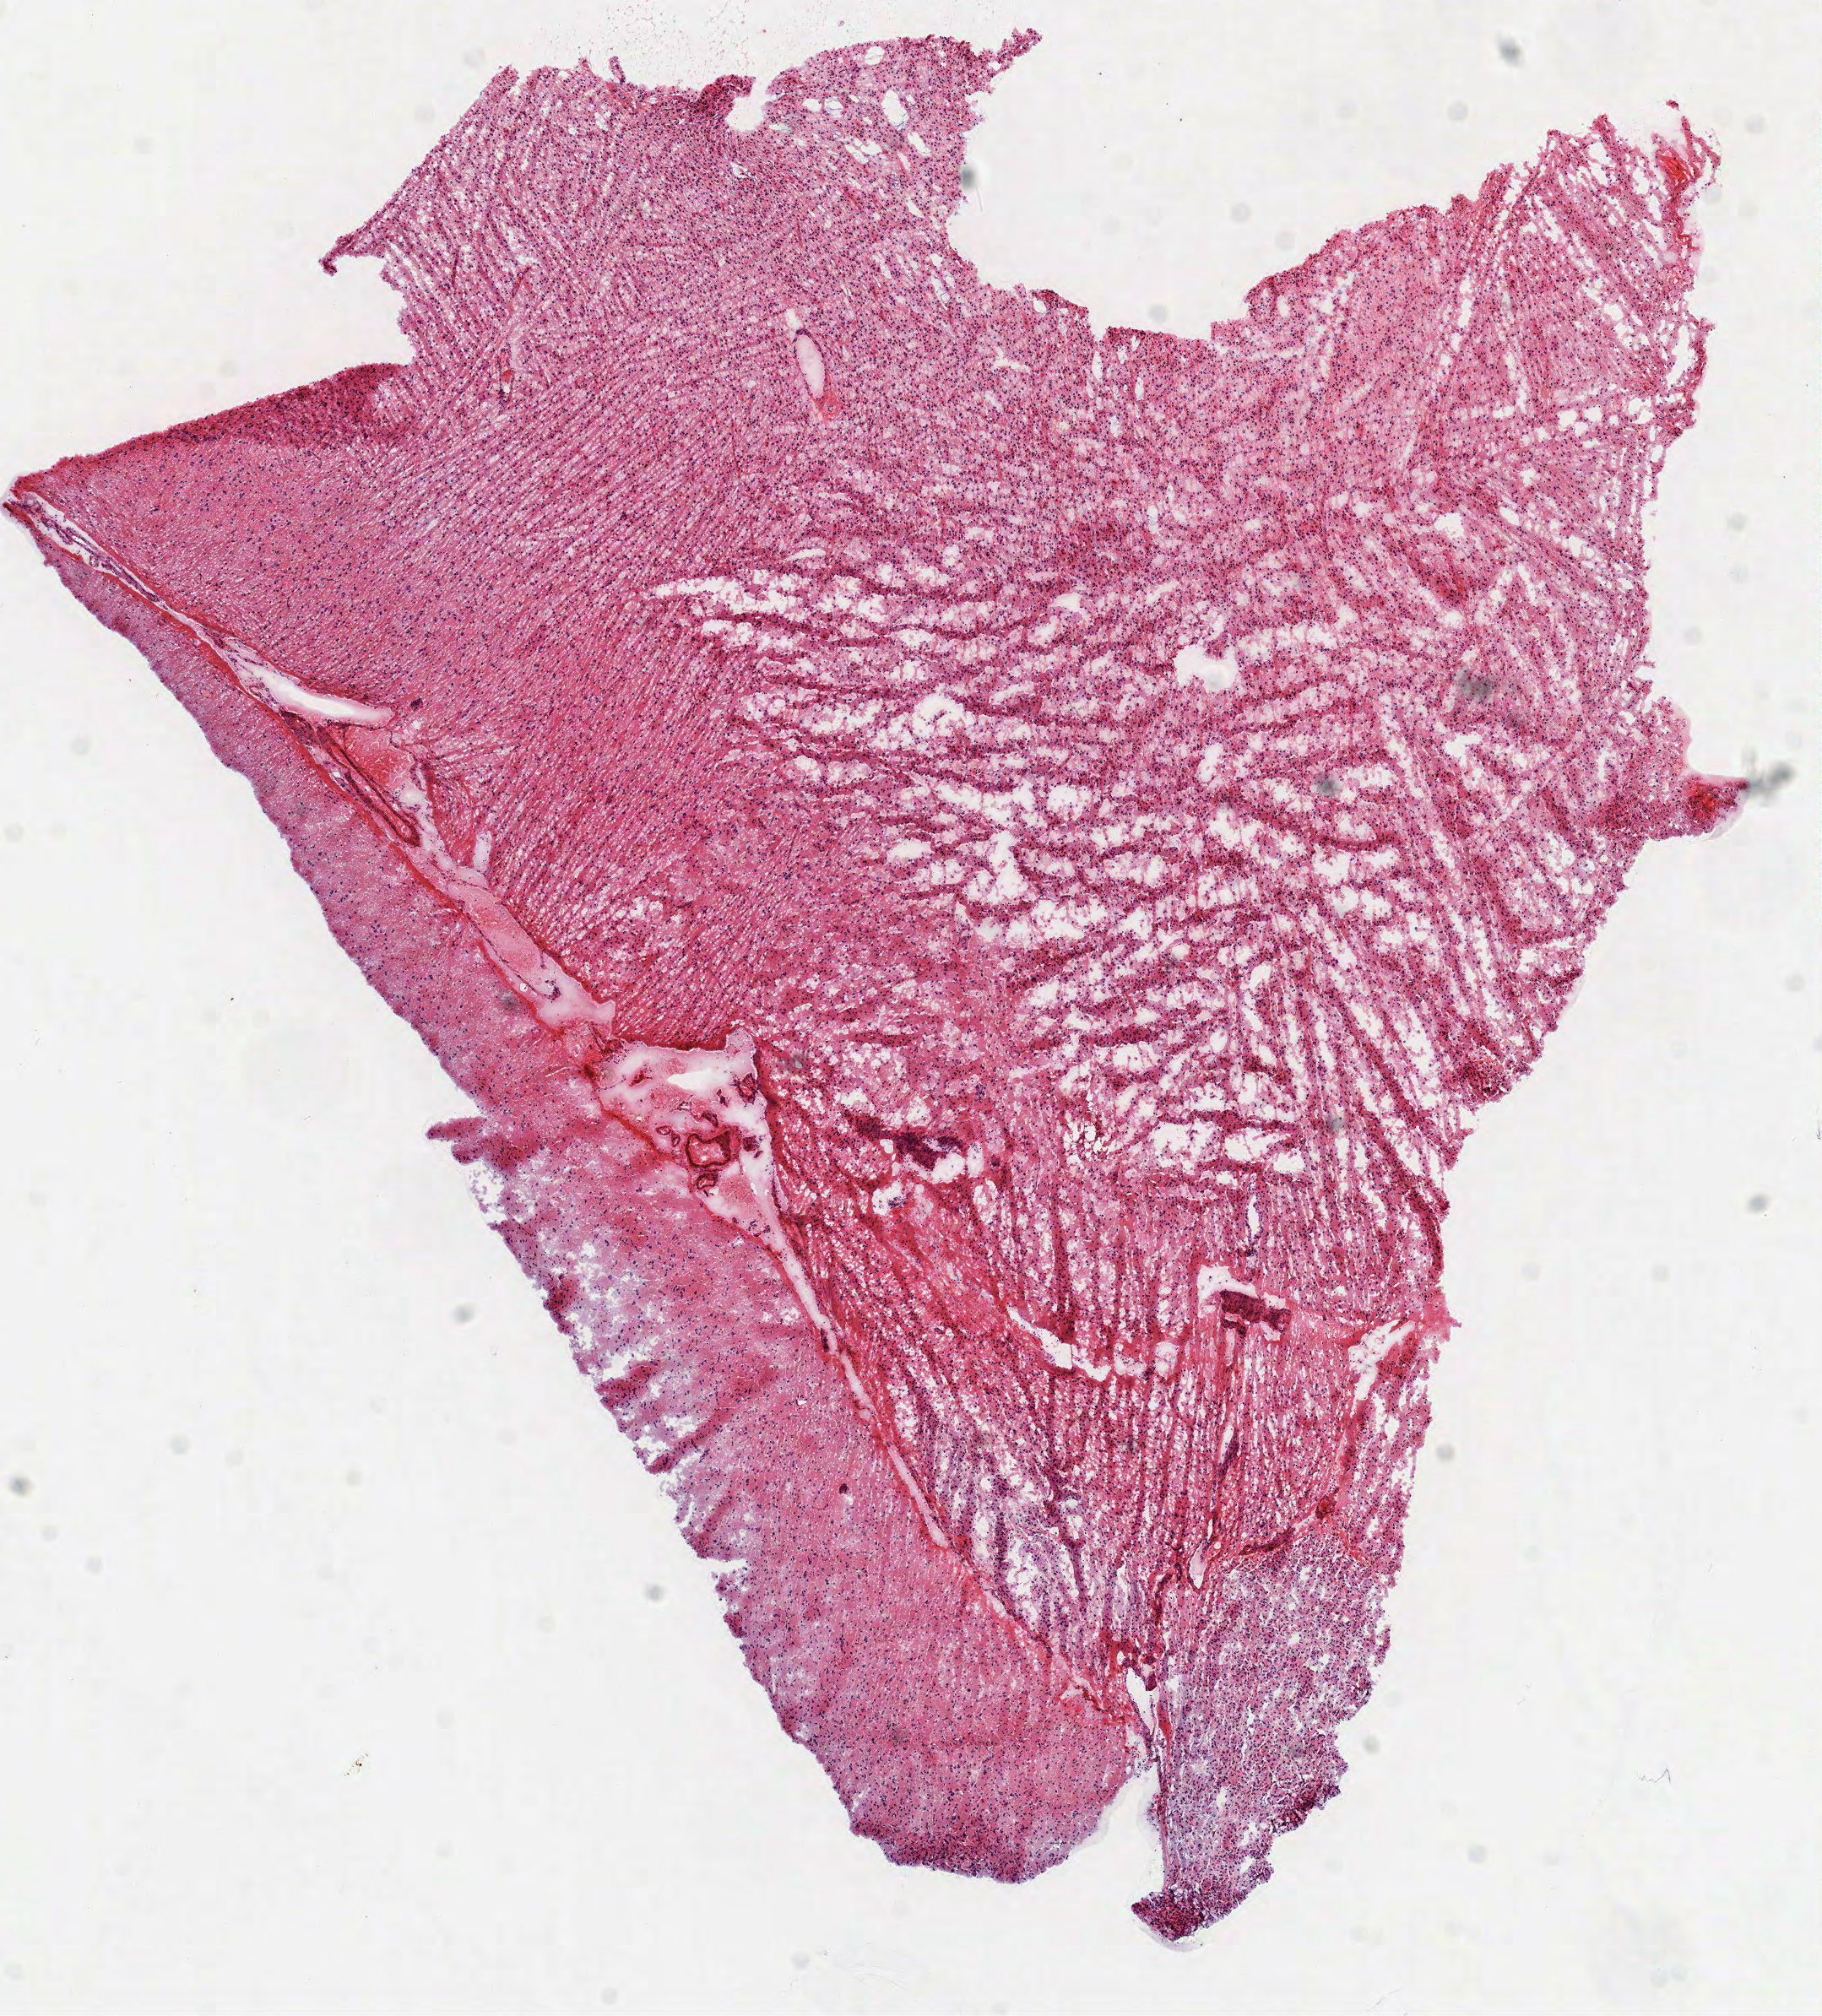
Whole-slide histology image, H&E — a low-resolution overview of the entire scanned area, about 8.7 x 9.6 mm. Frozen section from the top of the tissue portion. Sample: primary tumour, brain. Female patient; age at initial diagnosis 40 years. Histologic grade: G2 (moderately differentiated). Composition of this section per pathologist review: tumour cells 100%, tumour nuclei 75%, normal cells 0%, stromal cells 0%, necrosis 0%.
Pathologic diagnosis: Astrocytoma, NOS (cerebrum). Laterality: right.